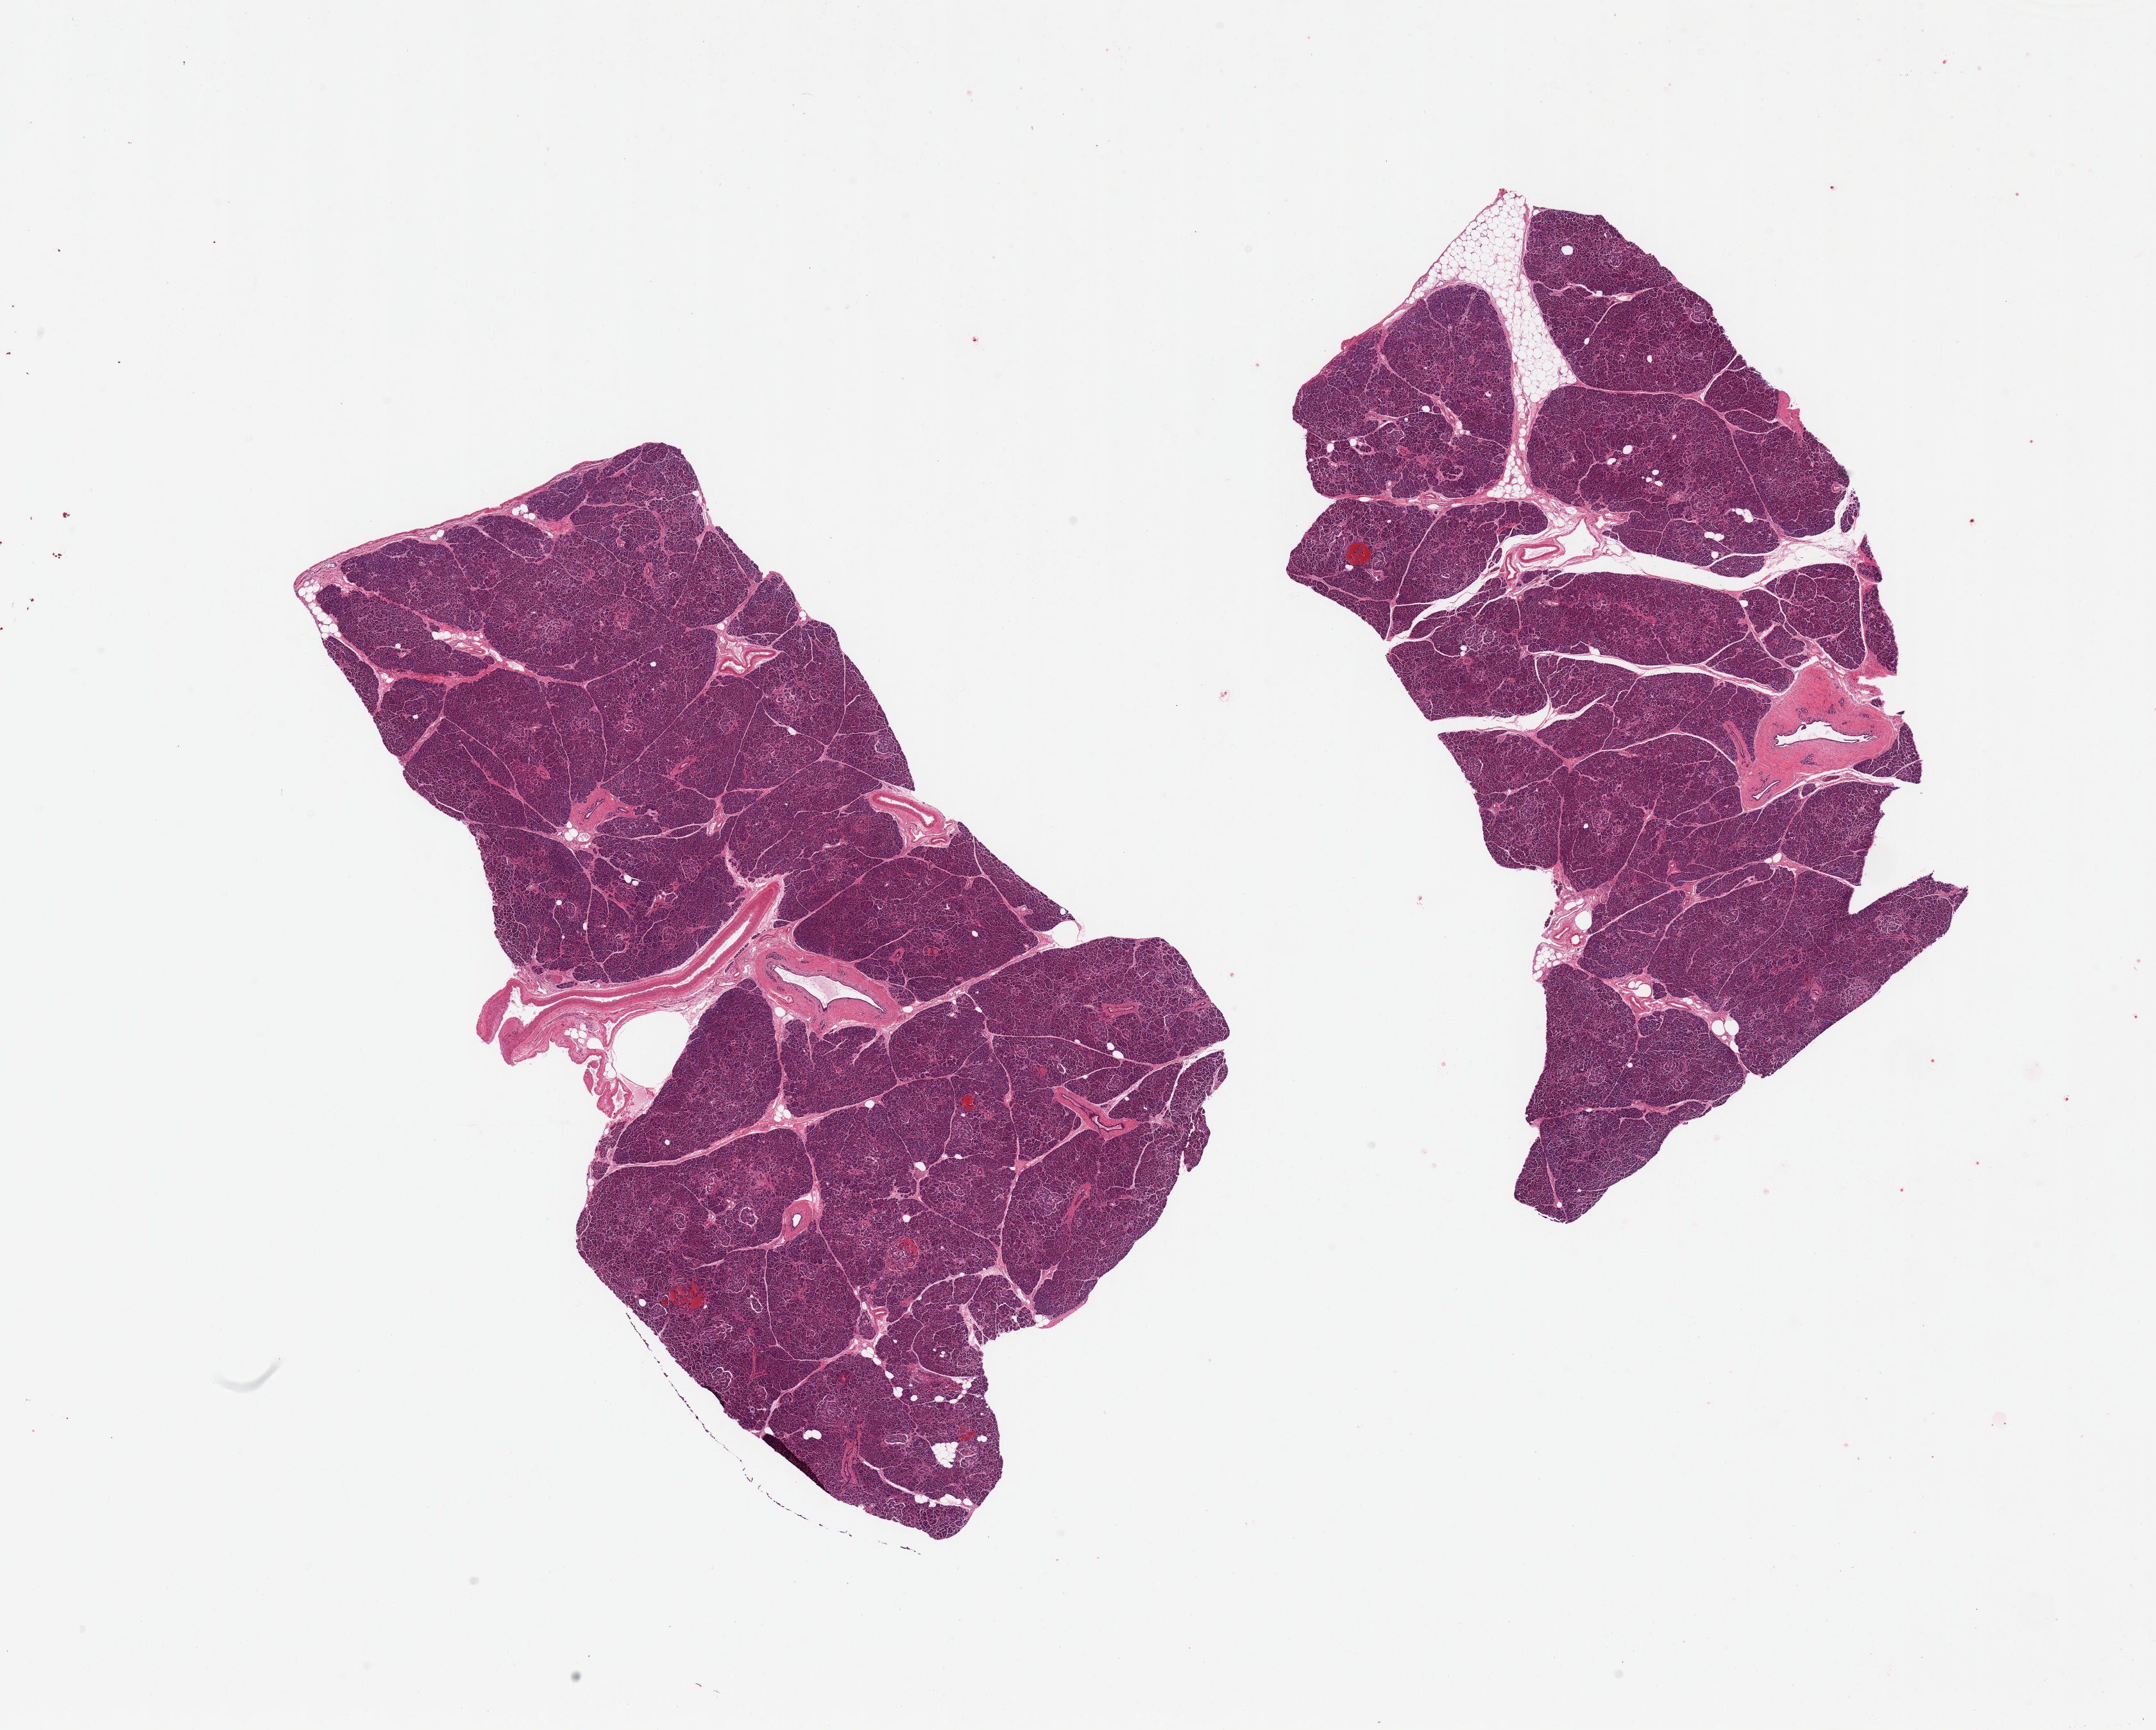
Whole-slide image, H&E stain, brightfield — low-resolution overview of the scanned area, about 26.6 x 21.3 mm (acquisition: 20x scan), PAXgene-fixed, paraffin-embedded tissue, section of pancreas (target tissue), tissue donor sample. Donor sex: male.
* pathologist's review note for this sample: 2 pieces; well preserved gland and Langerhans islets